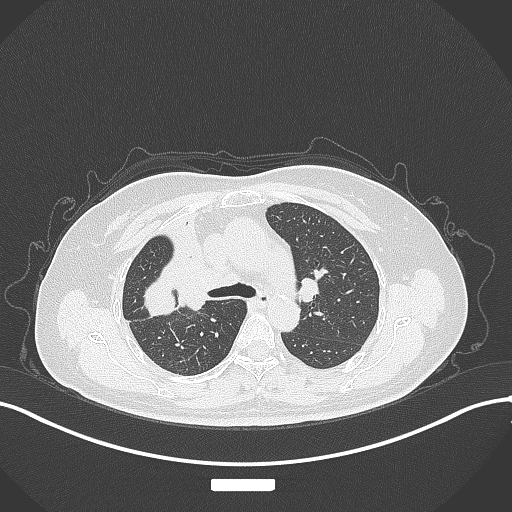
Chest CT, one axial slice. Slice 210 of 309 in the series (ordered by position). 120 kVp. Lung window (W 1500 / L -600 HU). 1 mm slice thickness. 512 × 512 image matrix. Female patient, age 60 years. From the clinical record (not read from this slice): clinical TNM (as recorded): T3 N1 M1.
Structures marked on this image (bounding box drawn by a radiologist):
- lung tumour (recorded histology: adenocarcinoma): box from (x=137, y=271) to (x=181, y=322) px